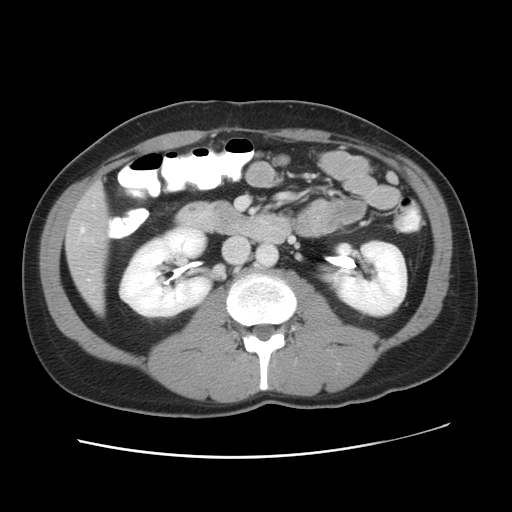
Contrast-enhanced abdominal CT, one axial slice. Position 18 of 49 along the scan axis. Reconstruction kernel STANDARD. Soft-tissue window (W 400 / L 40 HU). 5 mm slice thickness. 512 × 512 image matrix, field of view 363 × 363 mm. Male patient, age 41 years. From the clinical record (not read from this slice): diagnosis: colorectal cancer liver metastases, imaged before liver resection; multiple liver metastases: yes; largest metastasis: 0.7 cm; disease in both lobes: yes.
Structures marked on this image (expert manual segmentation):
- hepatic veins: bounding box [x1, y1, x2, y2] px = [80, 228, 85, 232]
- liver: [67, 186, 107, 310]